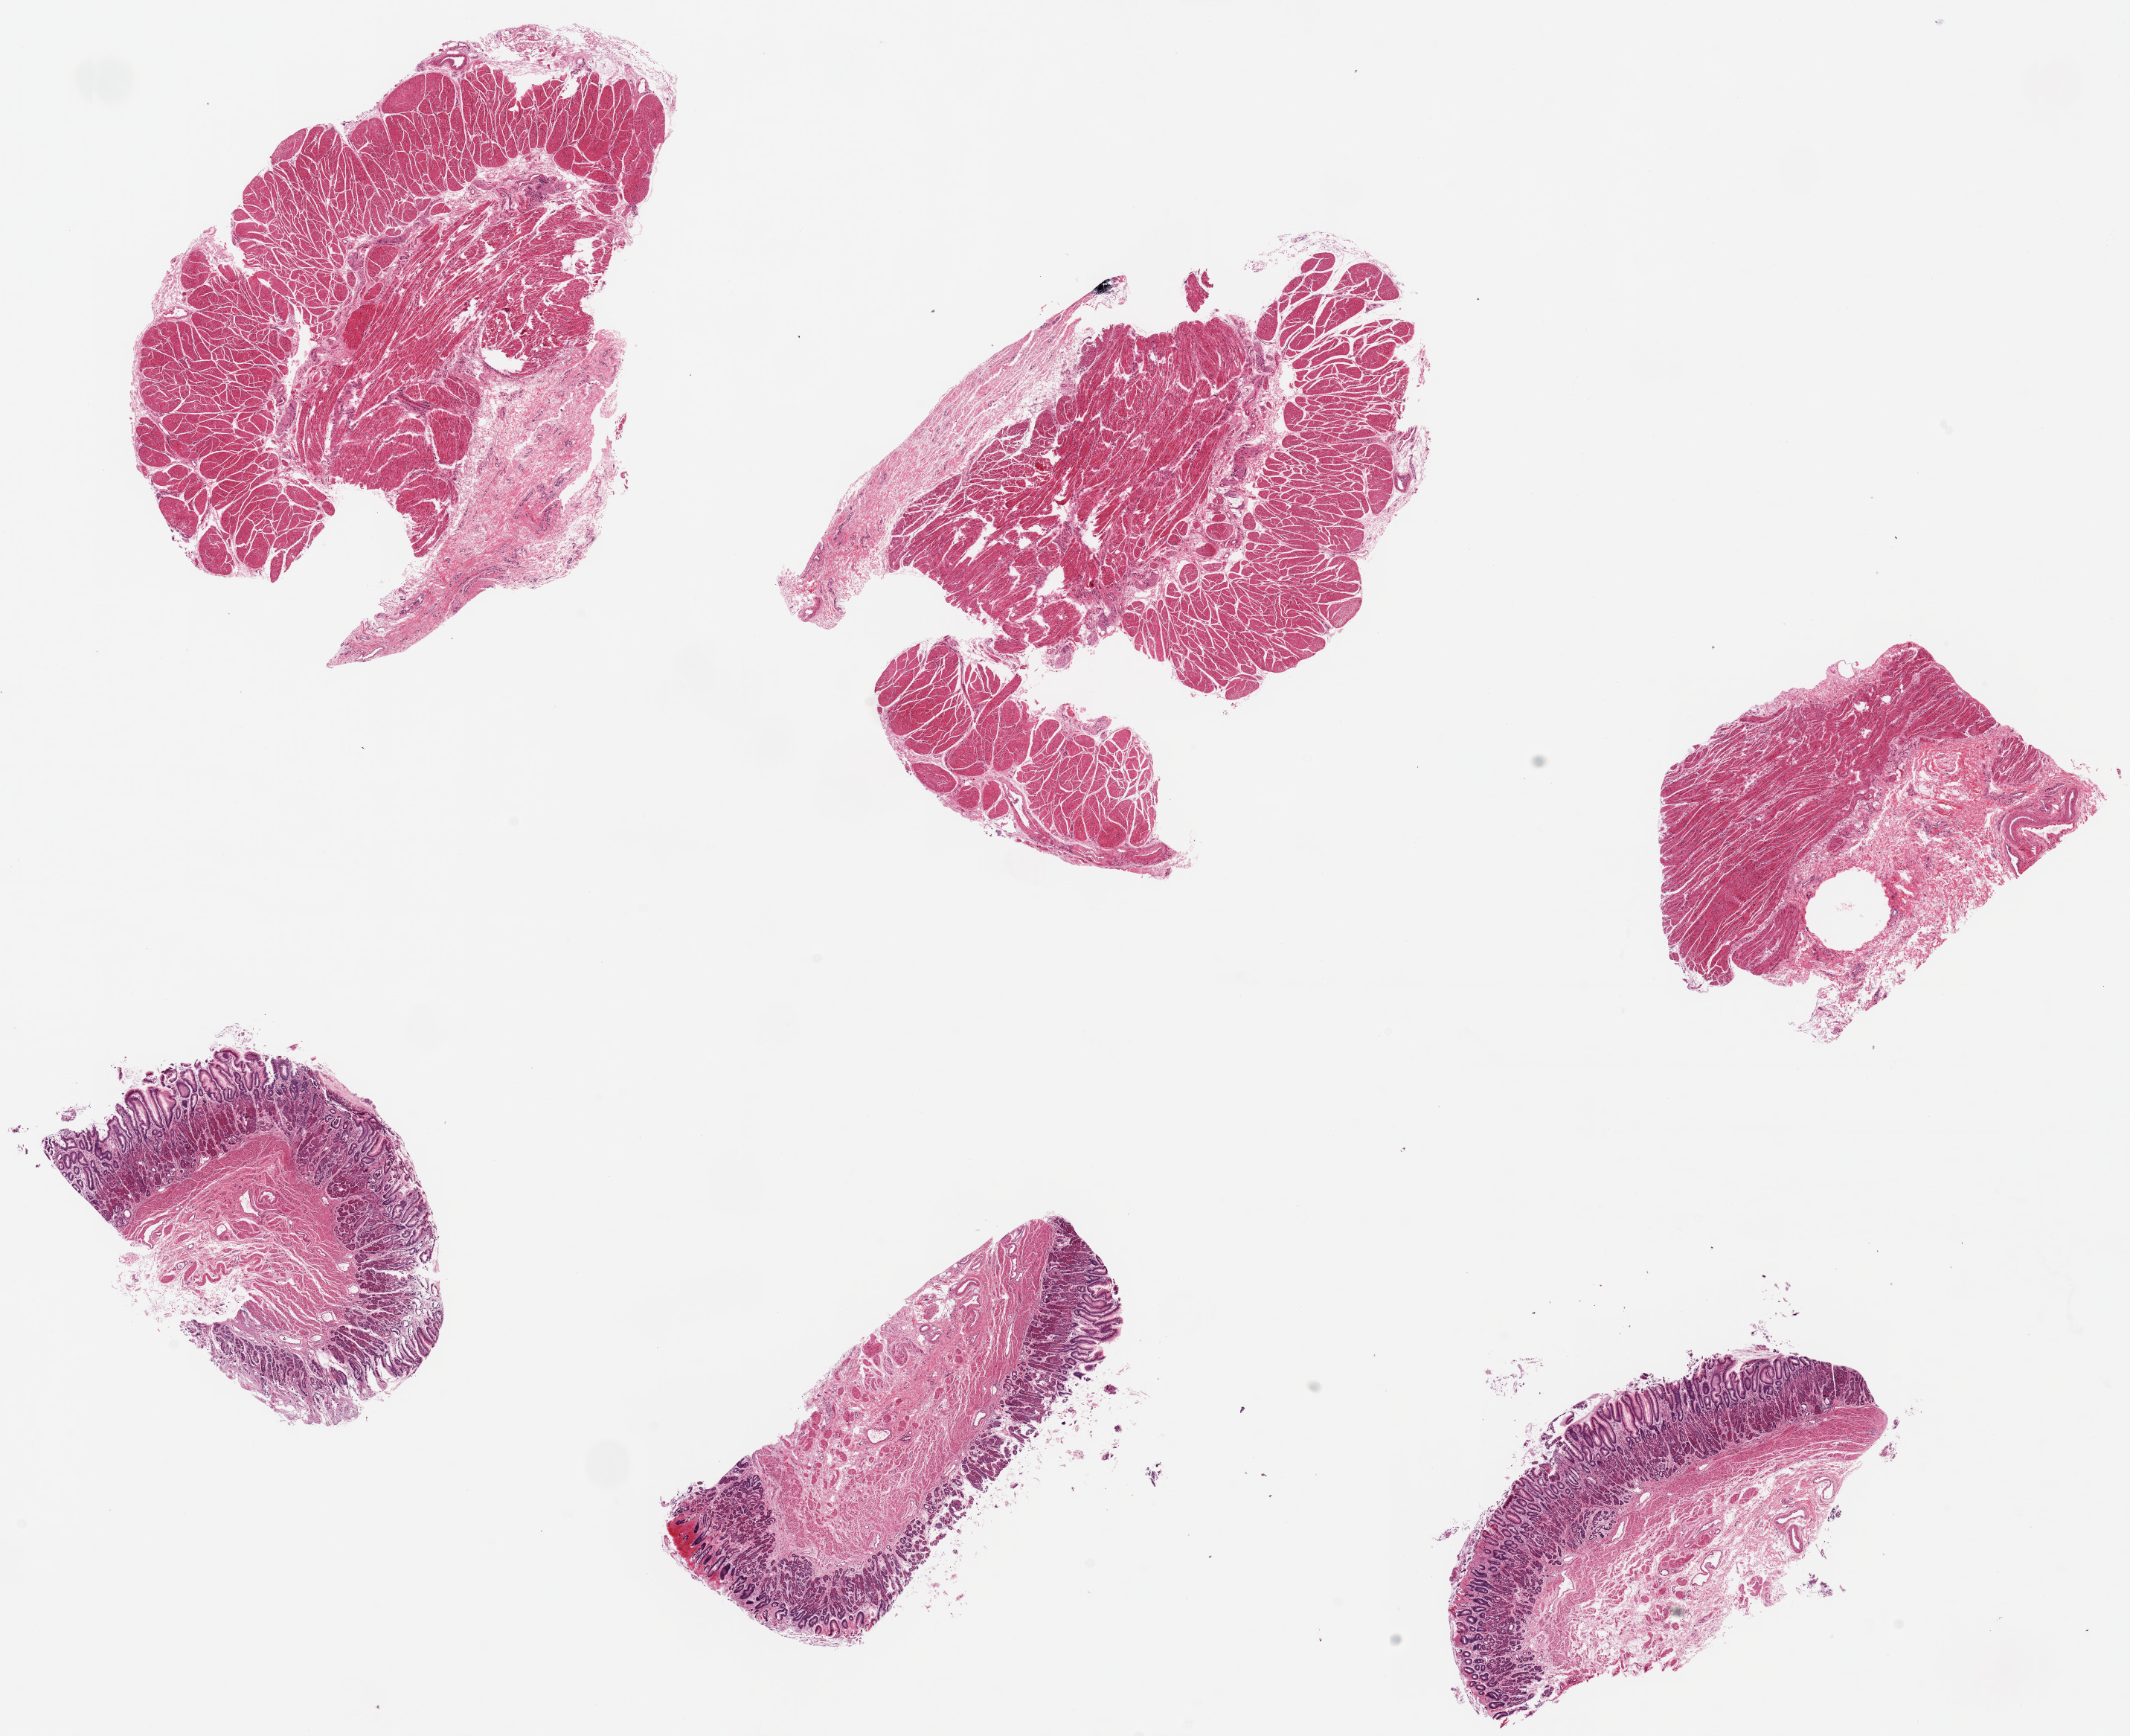
Hematoxylin and eosin (H&E) whole-slide image, low-resolution overview of the scanned area, about 22.6 x 18.5 mm, PAXgene-fixed paraffin-embedded (PFPE) section, target tissue: gastroesophageal junction, donor tissue sample. Male donor.
Review note (as recorded): 6 pieces, up to 7x5mm; 3 with muscle (target), 3 with fundic mucosa, no muscle.